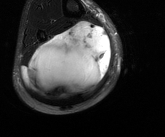
MRI of an extremity soft-tissue mass, one axial slice. Slice 65 of 81 in the series (ordered by position). T2-weighted fat-saturated. MR volume resampled by the dataset authors to the PET/CT grid (not the native acquisition matrix). 3.27 mm slice thickness. 165 × 137 image matrix. Male patient. Case-level facts recorded for this patient, not image findings: histological type: liposarcoma - round cell; grade: high; site of the primary tumour: right calf.
Annotated regions visible in this slice (expert contour drawn on MRI and transferred to this co-registered scan by the dataset authors):
- gross tumour volume (mass): bounding box [x1, y1, x2, y2] px = [21, 21, 111, 101]